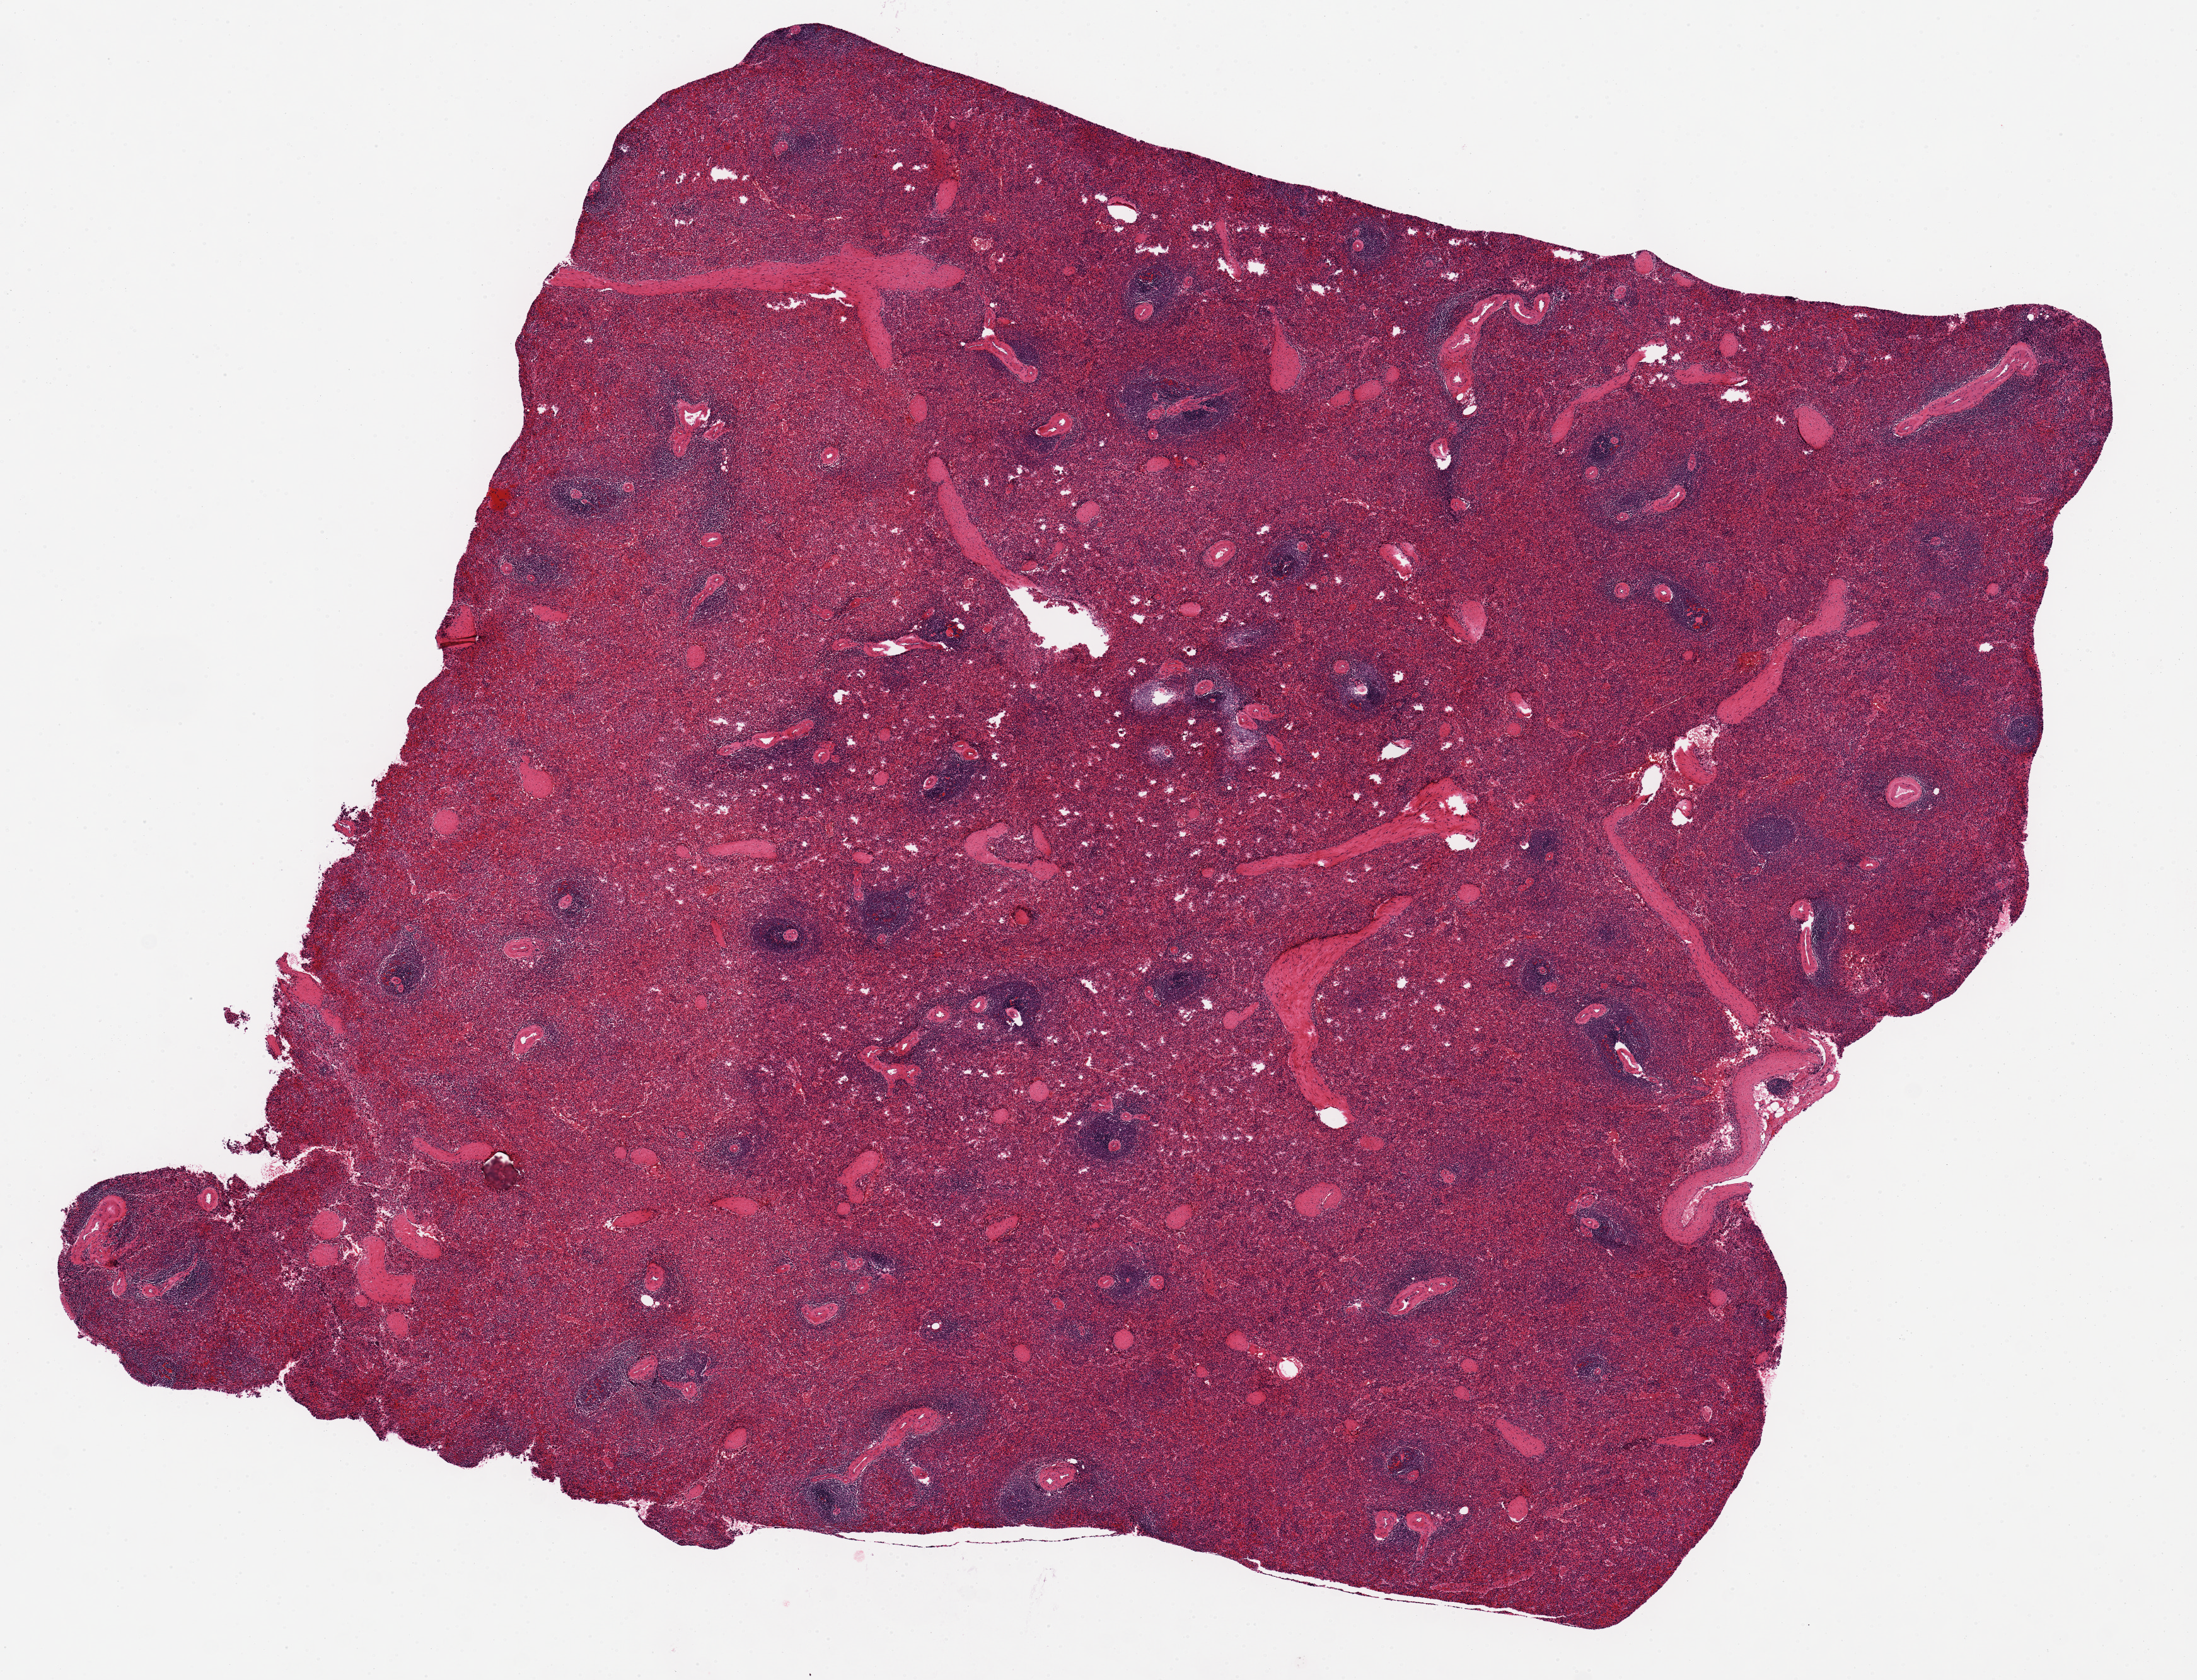
H&E whole-slide image, brightfield, shown as a low-resolution overview of the whole scanned area (about 13.8 x 10.5 mm, from a 20x scan), PAXgene-fixed paraffin-embedded (PFPE) section, sampled site (target tissue): spleen, donor tissue sample. Donor: female.
- reviewer comment on this tissue sample: Scattered fracture defects